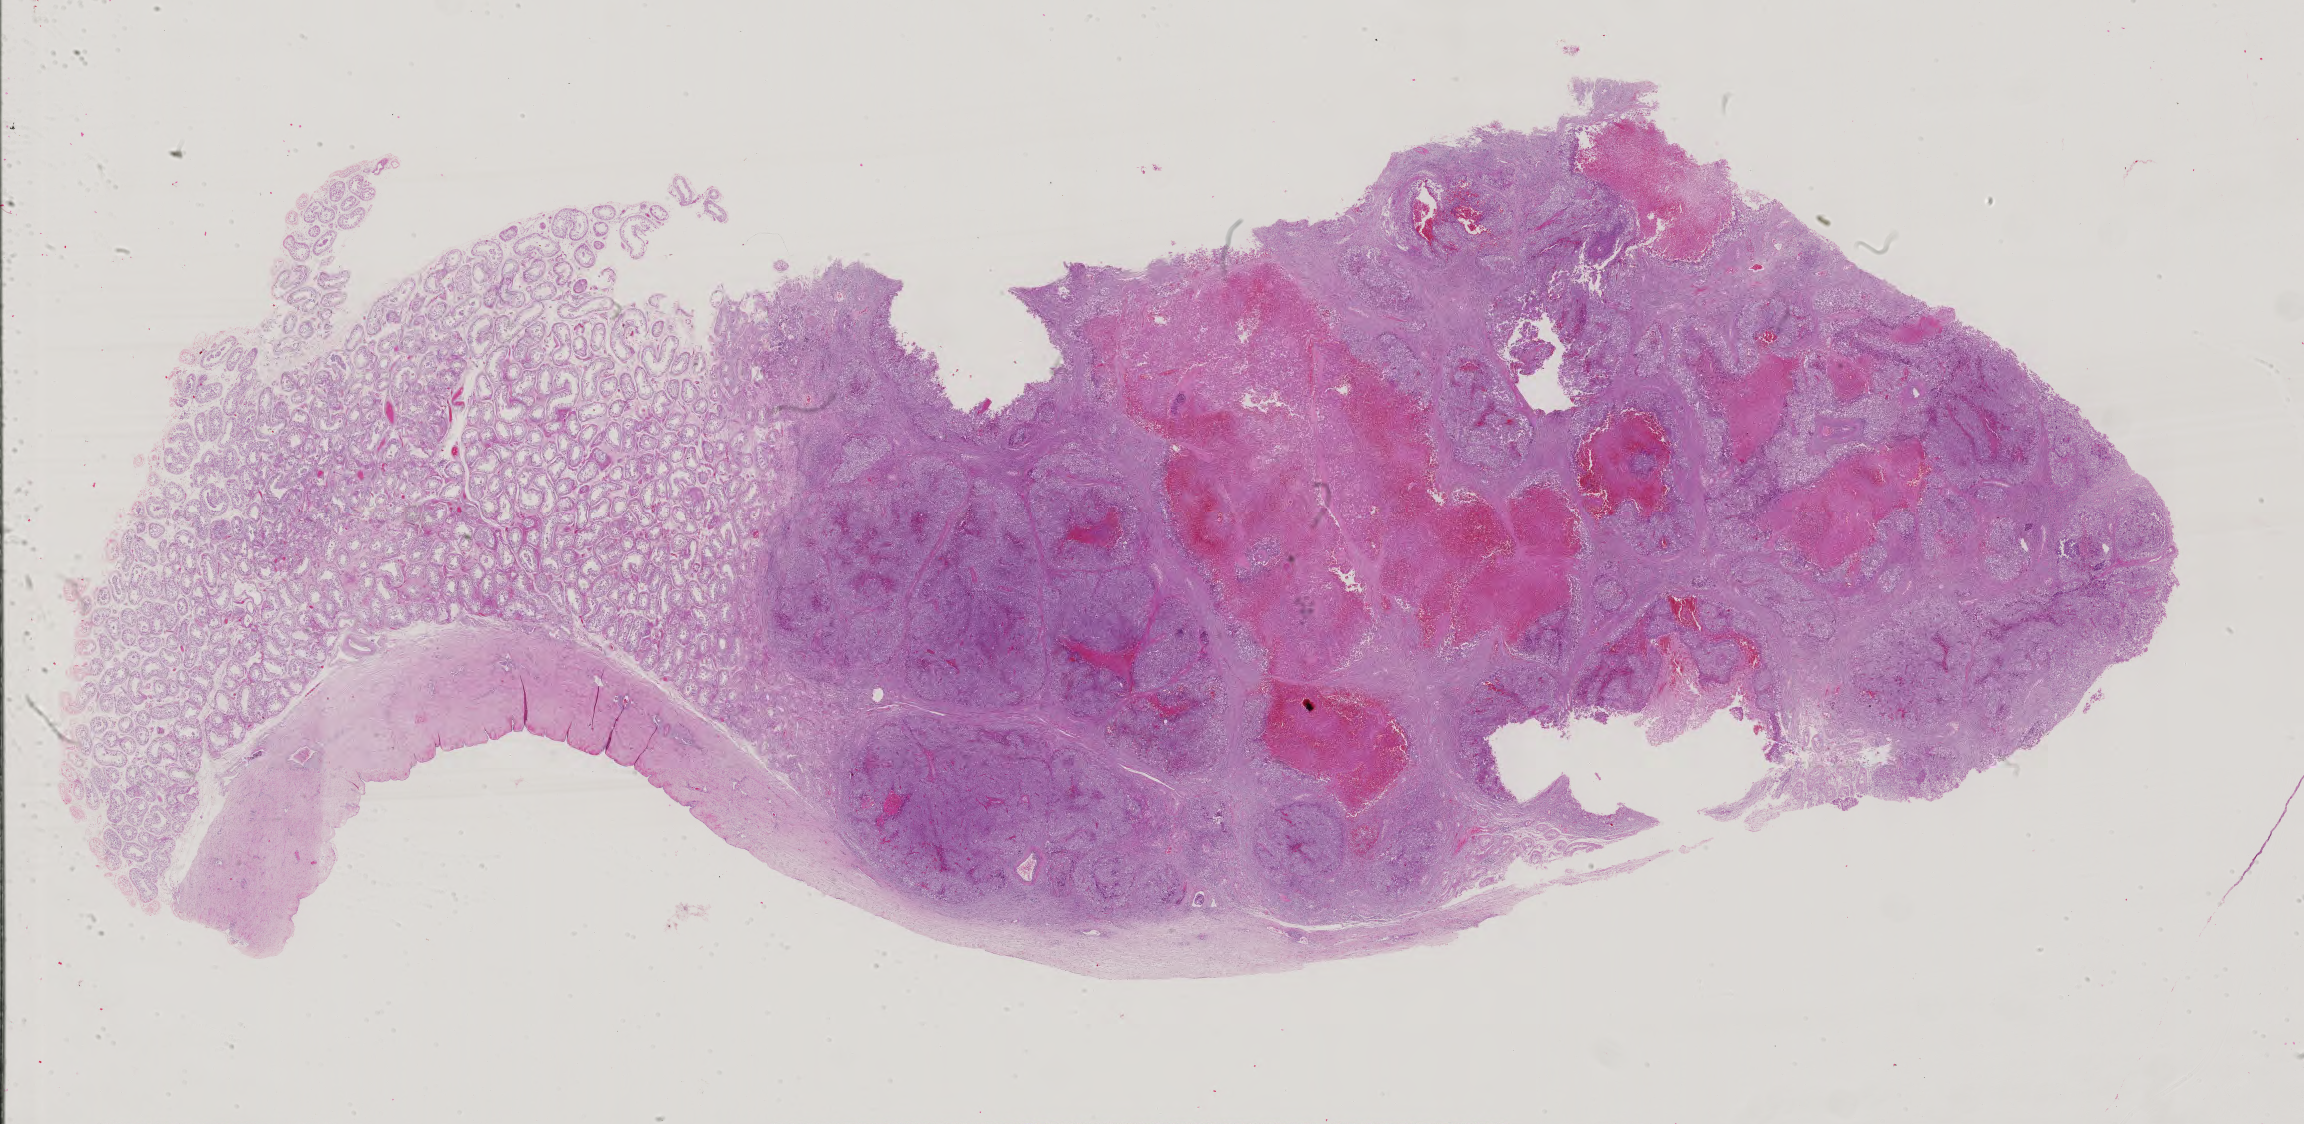
Hematoxylin and eosin (H&E) stained whole-slide image, a low-resolution overview of the entire scanned area, about 33.6 x 16.4 mm (from a 40x scan). Formalin-fixed paraffin-embedded (FFPE) diagnostic section. Sample: primary tumour, testis. Male, age 32 years at initial diagnosis.
AJCC pathologic stage: IS. Pathologic diagnosis: Embryonal carcinoma, NOS.